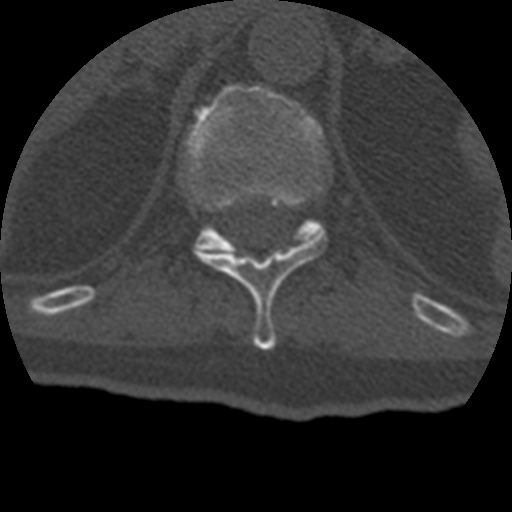
CT including the spine, one axial slice; slice 186 of 399 in the series (ordered by position); reconstruction kernel STANDARD; 120 kVp; bone window (W 1800 / L 400 HU); 1.25 mm slice thickness; 512 × 512 image matrix. Patient age 69 years. From the clinical record (not read from this slice): primary cancer: prostate.
Outlined on this slice (semi-automatically segmented with operator editing):
- T11 vertebra: box from (x=203, y=235) to (x=328, y=350) px
- T12 vertebra: (x=181, y=84)–(x=327, y=251)